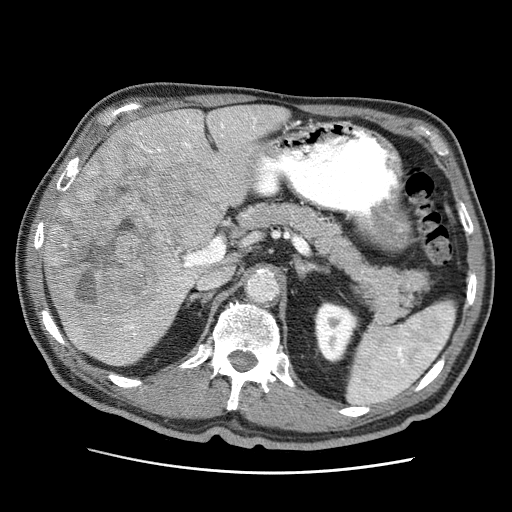
Contrast-enhanced abdominal CT (liver protocol), one axial slice; reconstruction kernel STANDARD; 120 kVp; soft-tissue window (W 400 / L 40 HU); 2.5 mm slice thickness; 512 × 512 image matrix, field of view 360 × 360 mm. From the clinical record (not read from this slice): diagnosis: hepatocellular carcinoma (patient treated with transarterial chemoembolisation; whether this scan precedes or follows treatment is not stated here); TNM stage (as recorded): Stage-IIIA; Child-Pugh class: A; tumour nodularity: multinodular; tumour size: 13.9 cm.
Outlined on this slice (semi-automatic segmentation, software-assisted and operator-edited):
- liver parenchyma outside the tumour (the mass and vessels are separate outlines, so this box may not span the whole liver): bounding box [x1, y1, x2, y2] px = [44, 104, 288, 366]
- mass: [48, 137, 215, 348]
- liver vessels: [75, 114, 257, 363]